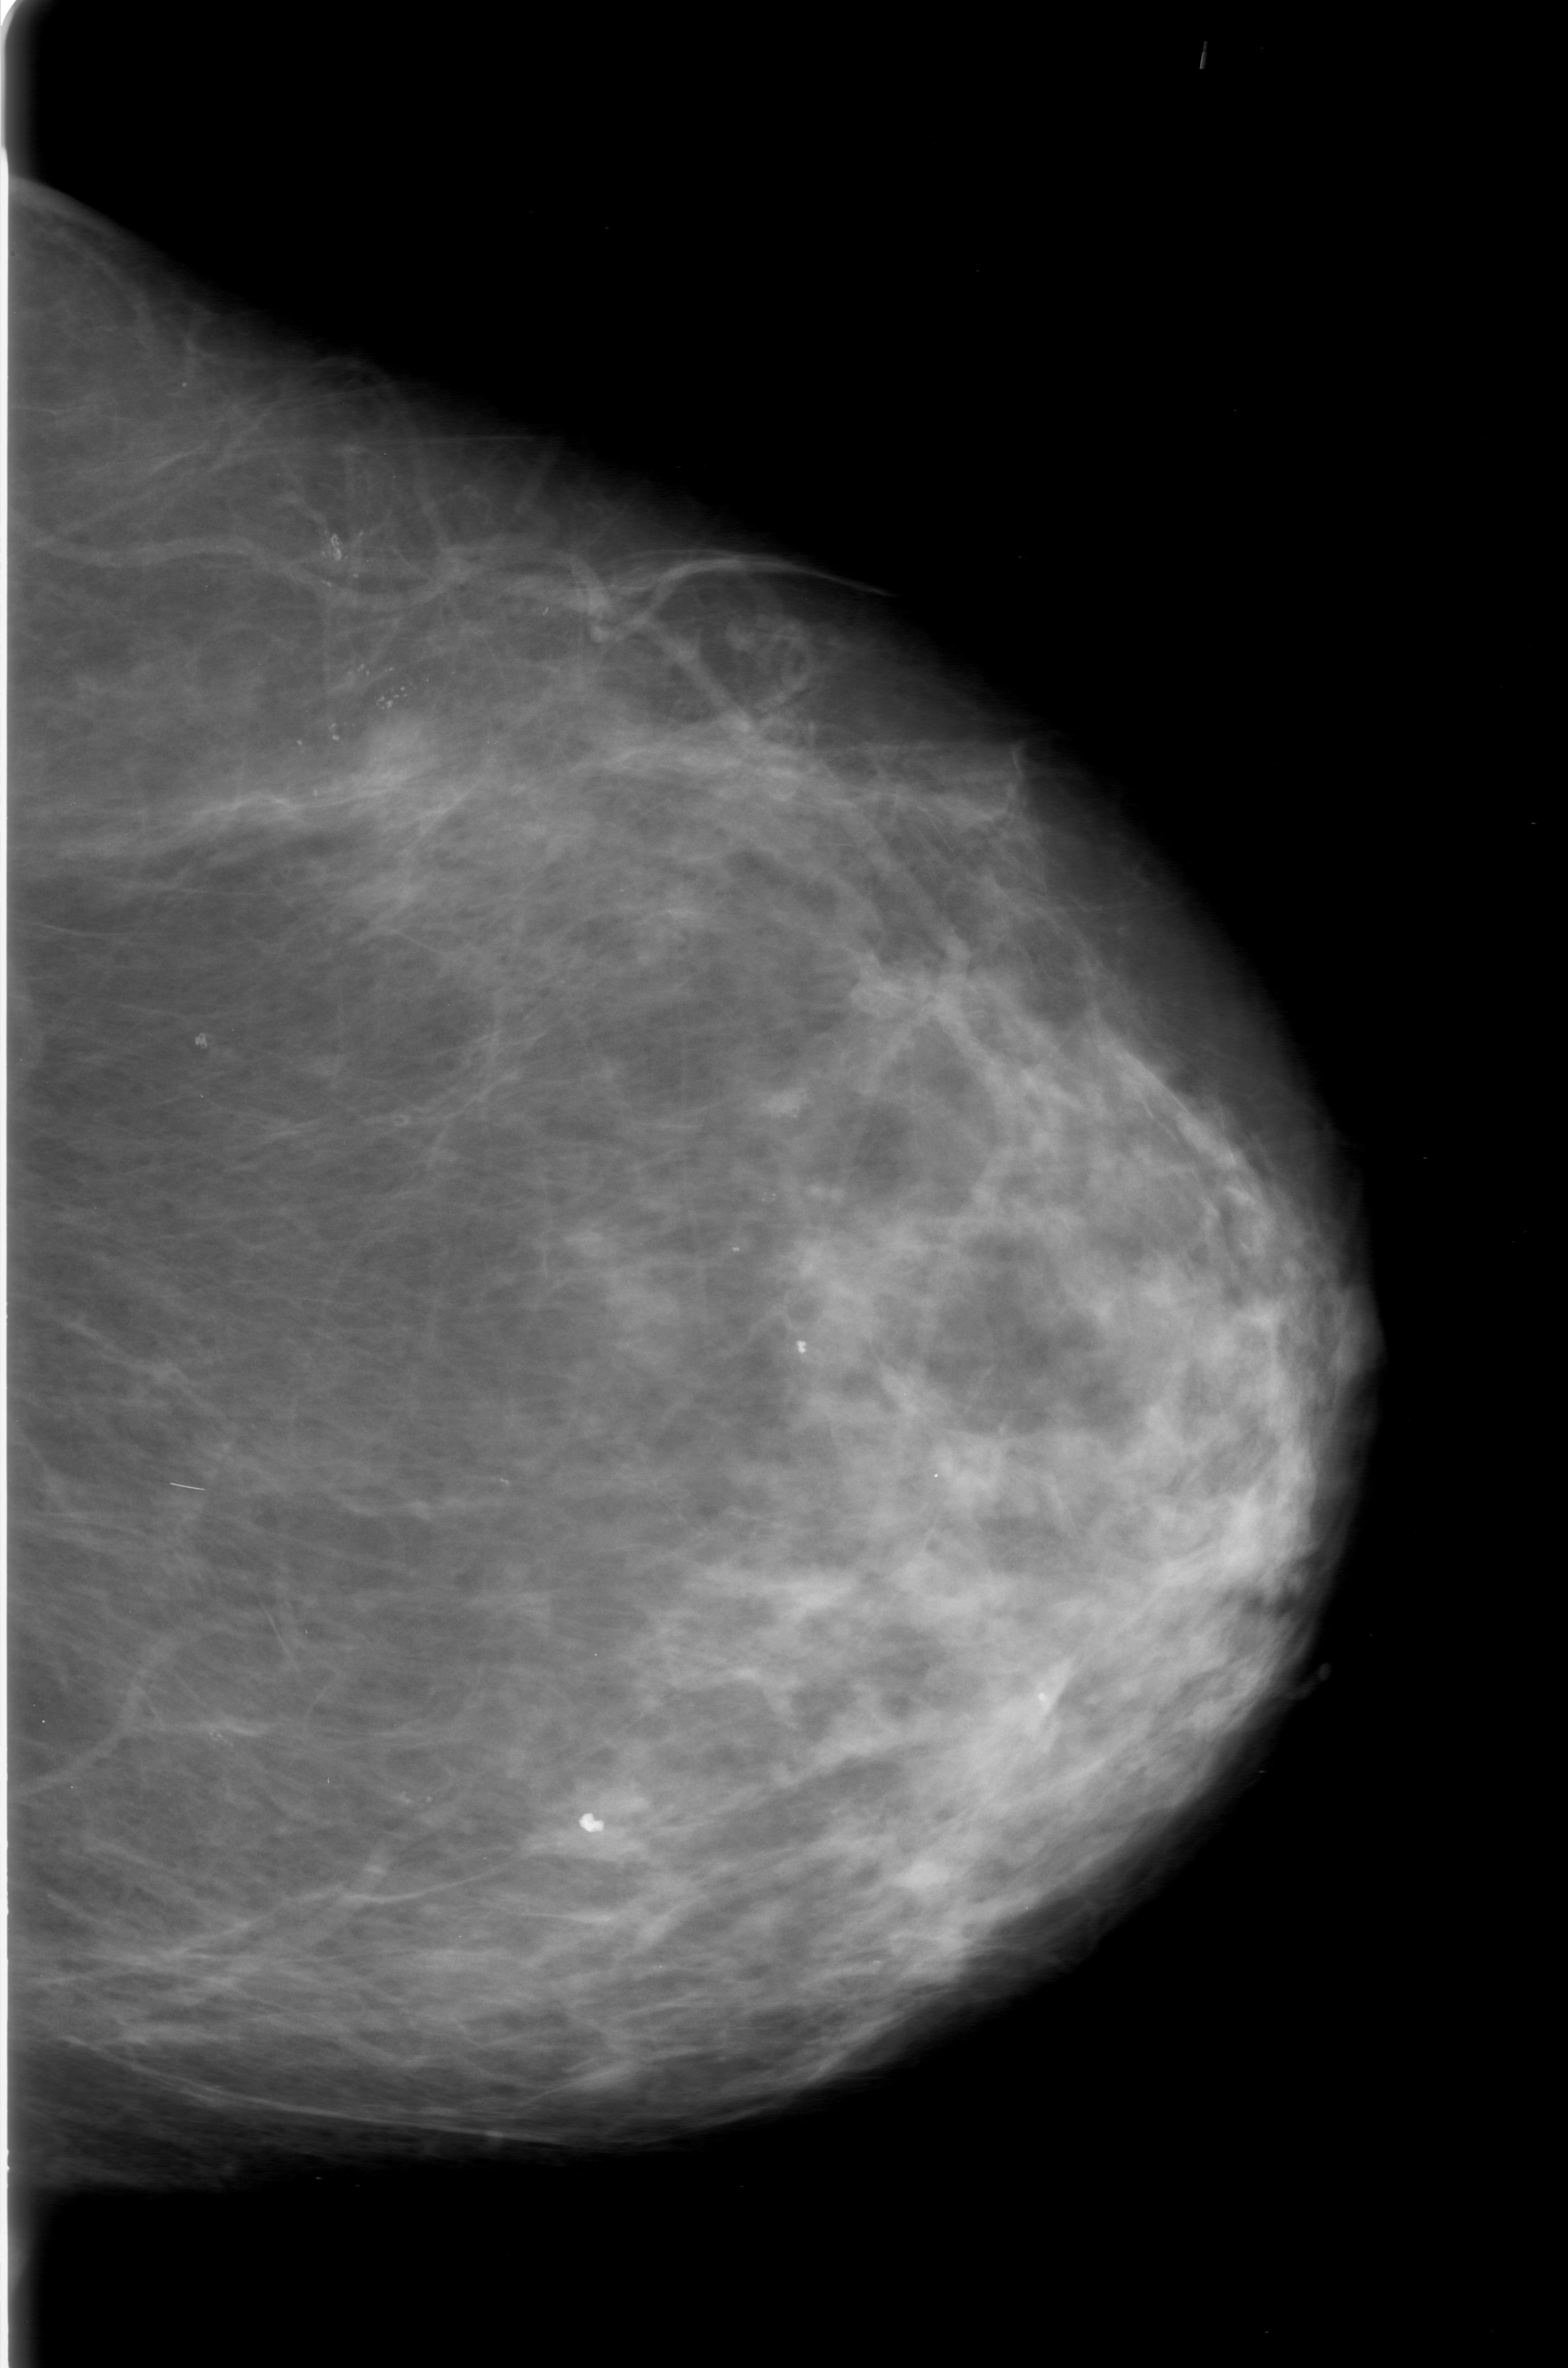
Scanned film-screen mammogram, left breast, CC view, BI-RADS breast density category 2 (scale 1–4).
- Marked findings (only marked abnormalities are described; nothing is implied about the rest of the image): calcifications, morphology round and regular / pleomorphic, distribution clustered; BI-RADS assessment category 0 (incomplete: needs additional imaging); pathology result (as recorded, not read from the image): benign.